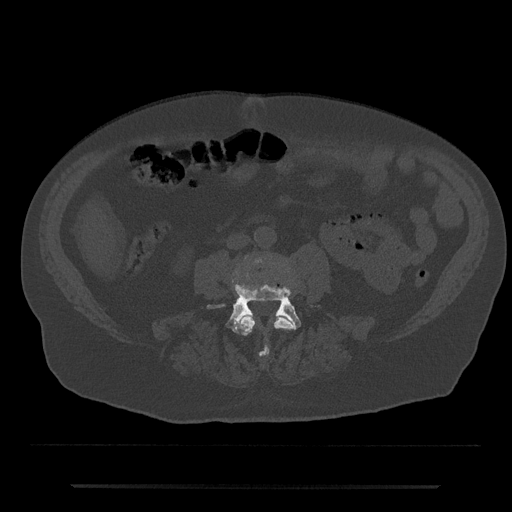
CT including the spine, one axial slice; slice 371 of 797 in the series (ordered by position); reconstruction kernel Br40s/3; 120 kVp; bone window (W 1800 / L 400 HU); 0.5 mm slice thickness; 512 × 512 image matrix. Male patient, age 80 years. Case-level facts recorded for this patient, not image findings: primary cancer: prostate.
Annotated regions visible in this slice (semi-automatic segmentation, software-assisted and operator-edited):
- L3 vertebra: box from (x=236, y=258) to (x=294, y=356) px
- L4 vertebra: (x=207, y=283)–(x=301, y=332)